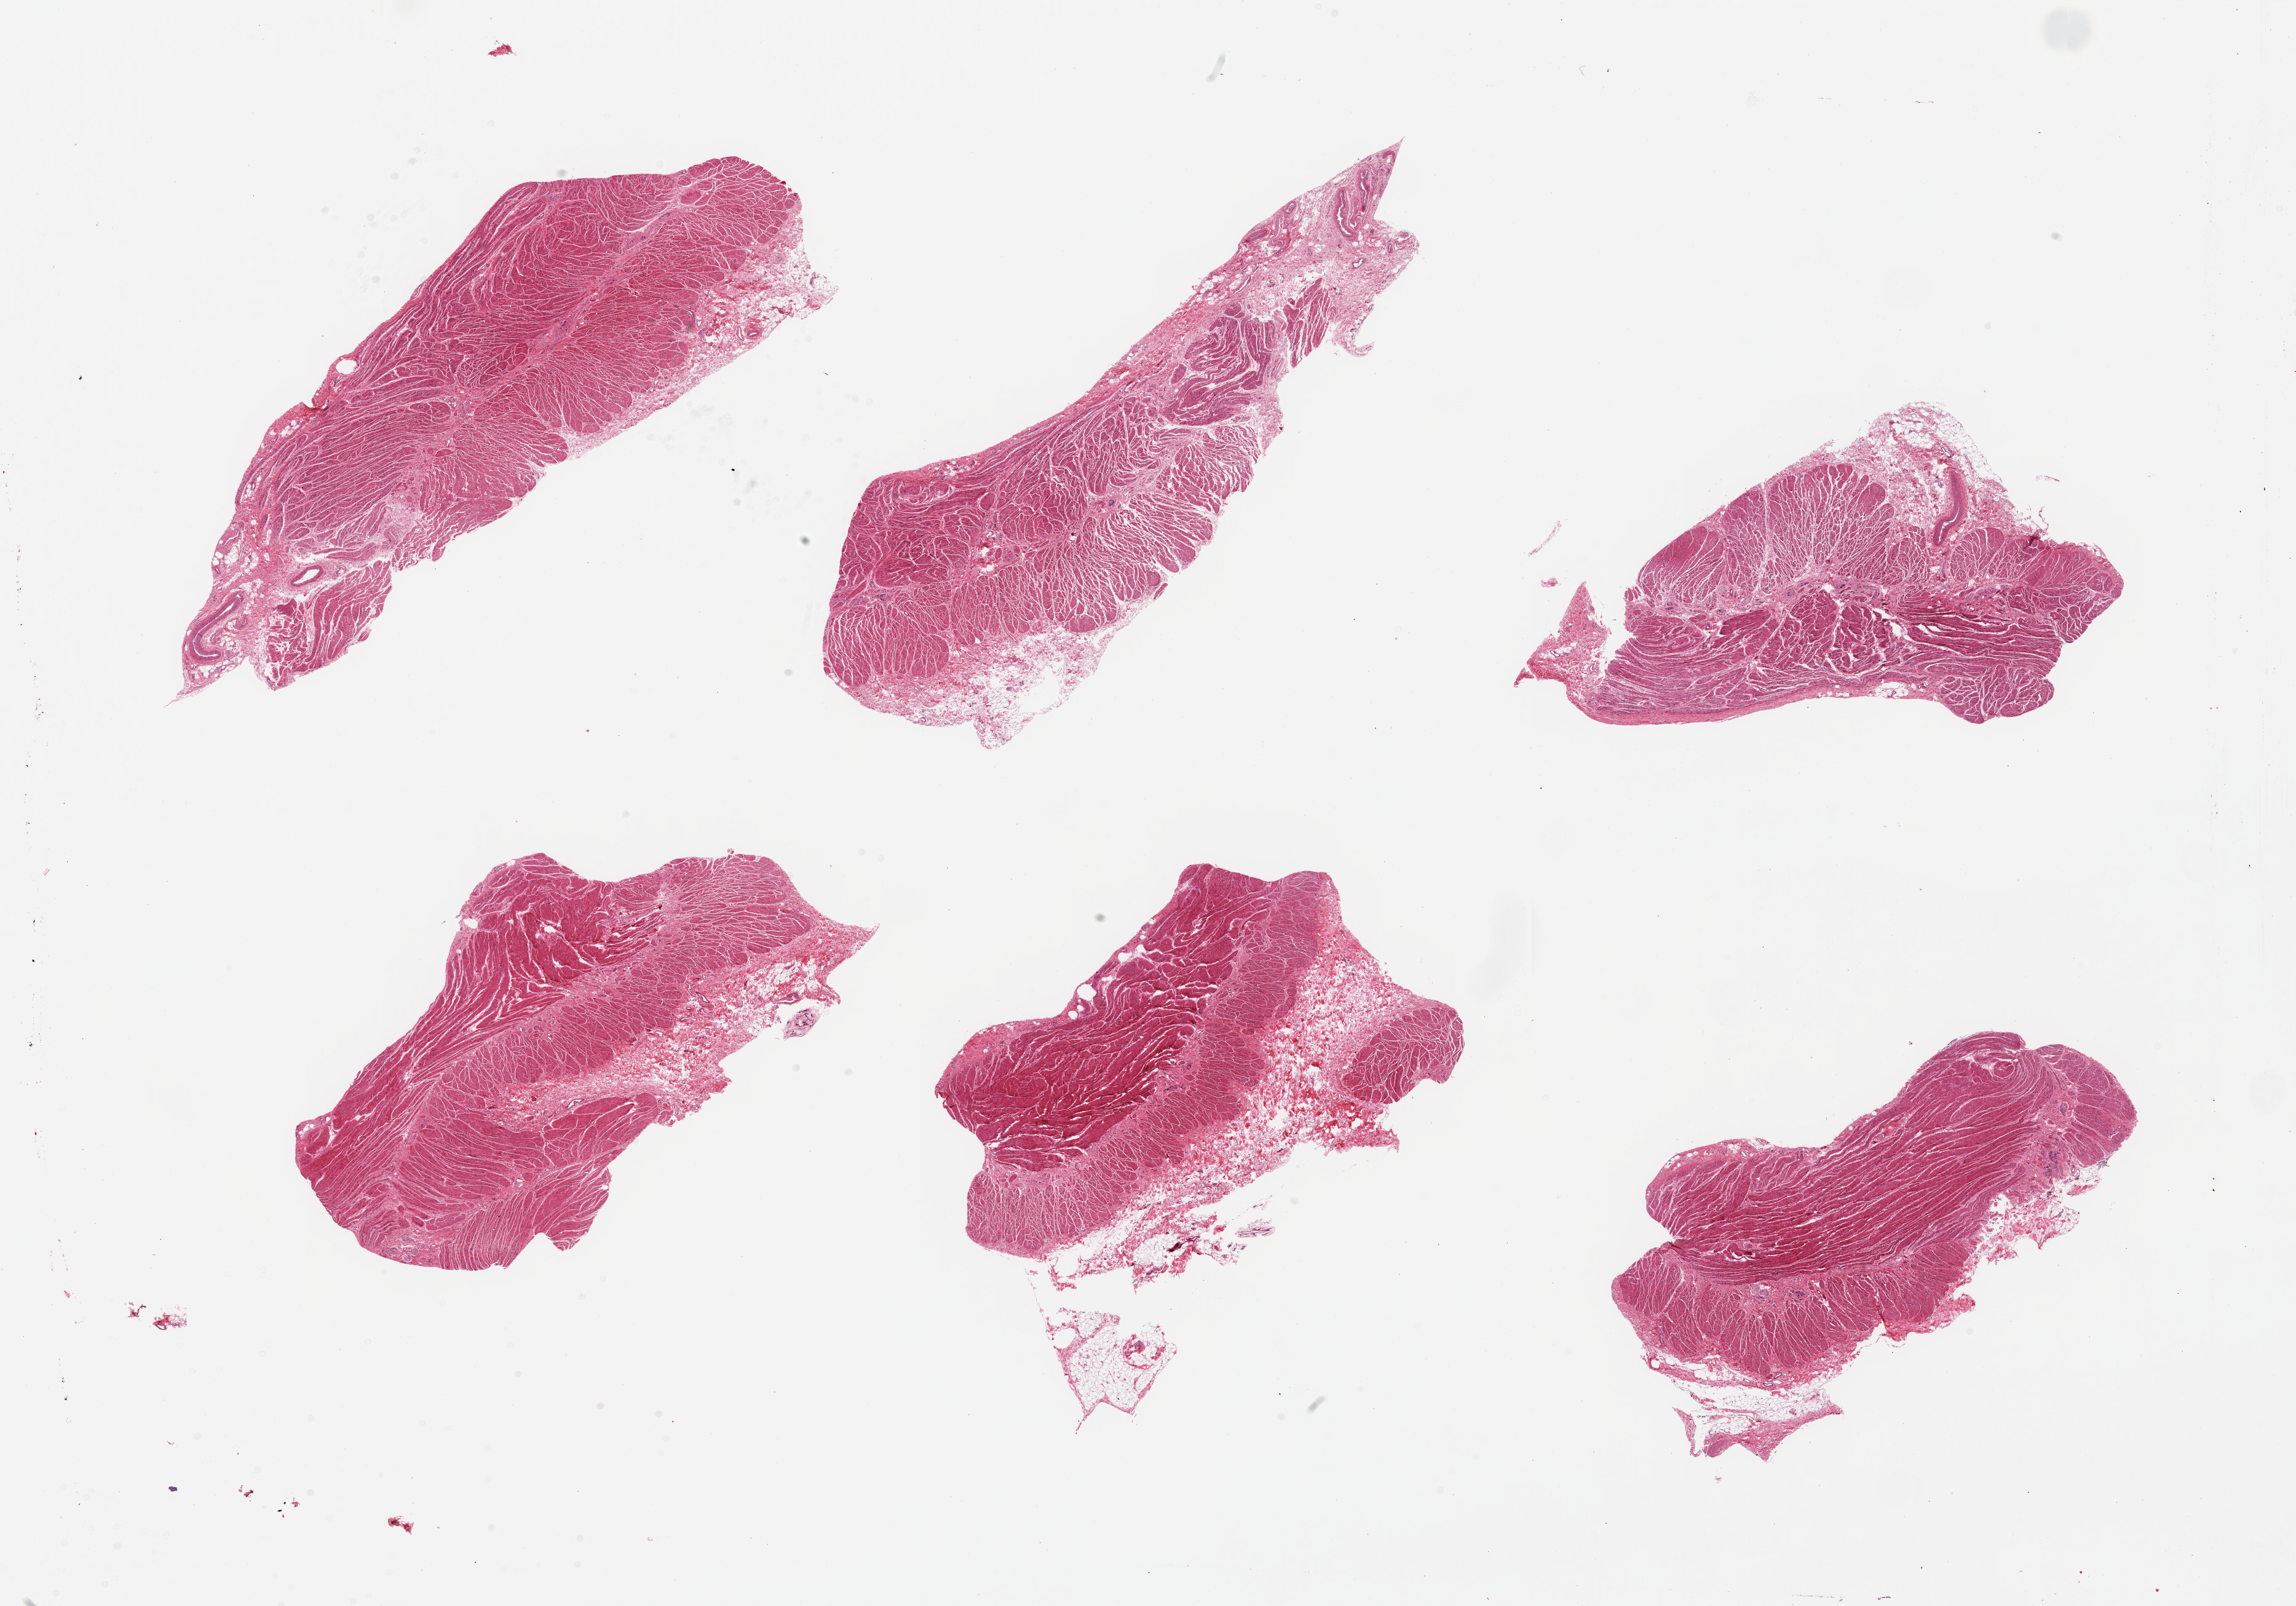
Digitized haematoxylin and eosin-stained section, brightfield, whole scanned area (about 29.5 x 20.7 mm, acquisition: 20x scan) shown as a low-resolution overview; PAXgene-fixed, paraffin-embedded tissue; sampled site (target tissue): gastroesophageal junction; tissue donor sample.
Reviewer comment on this tissue sample: 6 pieces, confirmed taret muscularis.